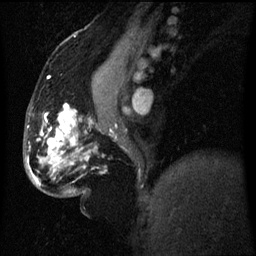
Breast MRI (dynamic contrast-enhanced), one sagittal slice; slice 28 of 60 in the series (ordered by position); dynamic contrast-enhanced series, image 2 of 3 at this slice position (ordered by acquisition); 1.5 T; TE 4.2 ms, TR 8 ms; 2.5 mm slice thickness; 256 × 256 image matrix. Patient: female, 50 years.
Outlined on this slice (semi-automatic segmentation, software-assisted and operator-edited):
- analysis volume of interest (the breast-tissue region the enhancement analysis was run in; not a lesion): bounding box [x1, y1, x2, y2] px = [48, 150, 58, 165]
- tumour enhancement mask (voxels above the 70 % enhancement threshold inside the analysis volume of interest): [49, 150, 51, 153]